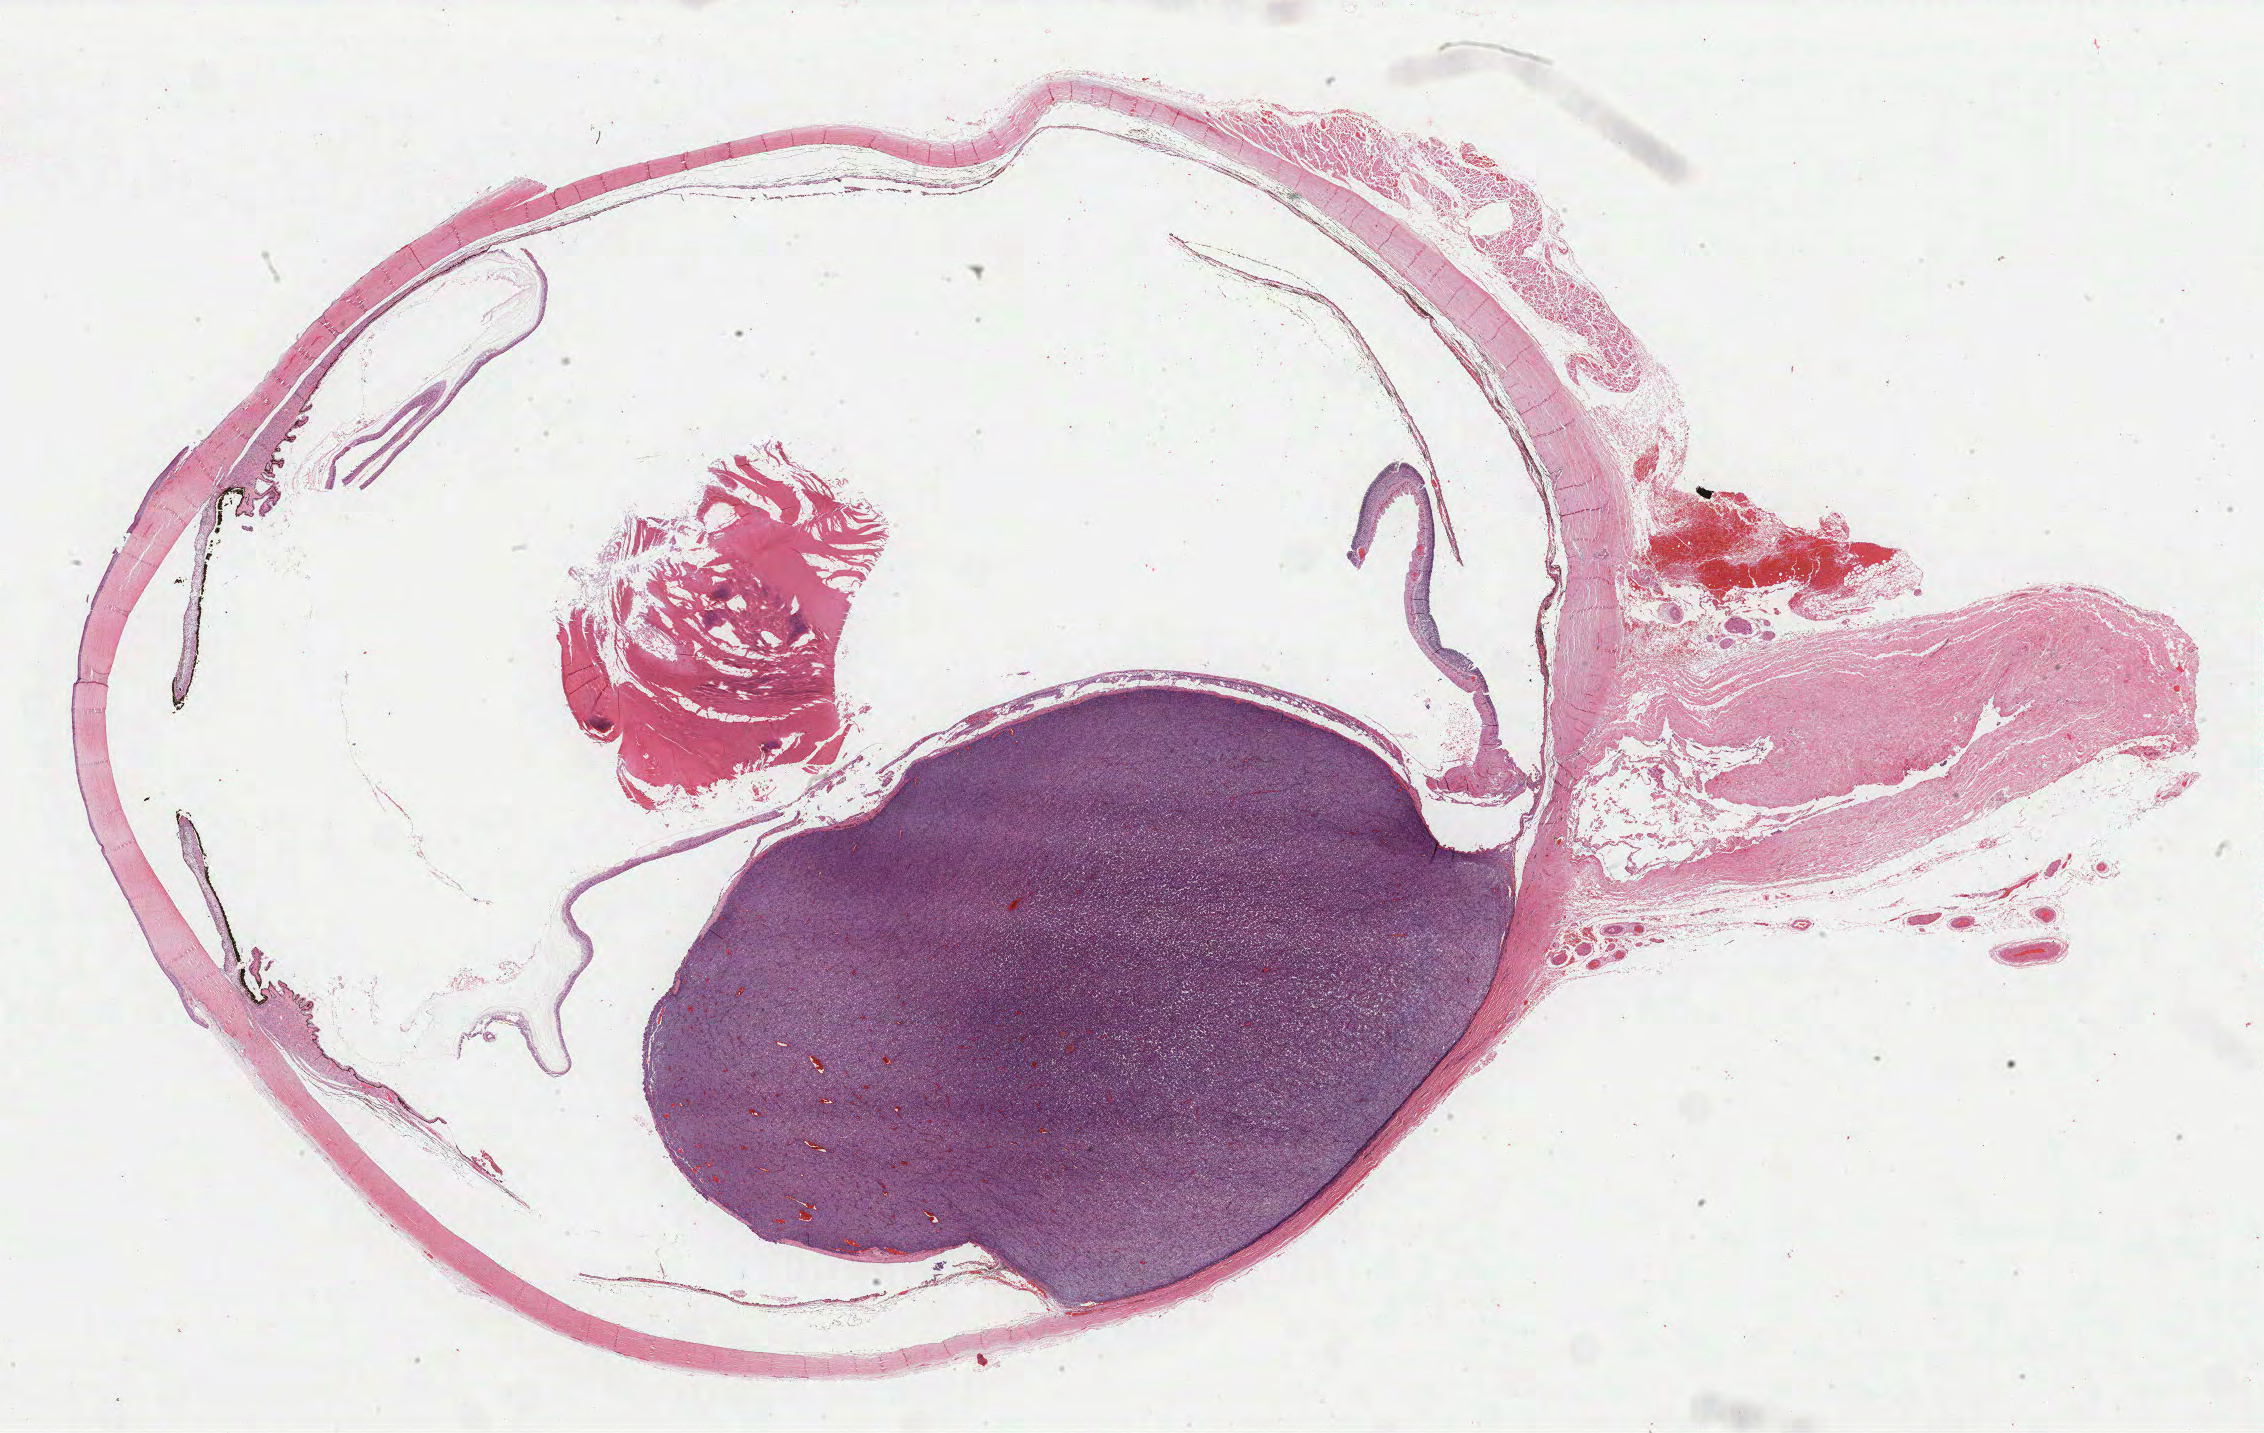
Digitized H&E tissue section (whole slide) — a low-resolution overview of the entire scanned area, about 35.8 x 22.7 mm (from a 40x scan). Formalin-fixed paraffin-embedded (FFPE) diagnostic section. Uvea, primary tumour sample. Female, age 51 years at initial diagnosis.
• histologic diagnosis: Epithelioid cell melanoma (choroid)
• TNM: T3a NX MX
• AJCC pathologic stage: IIB (7th edition)